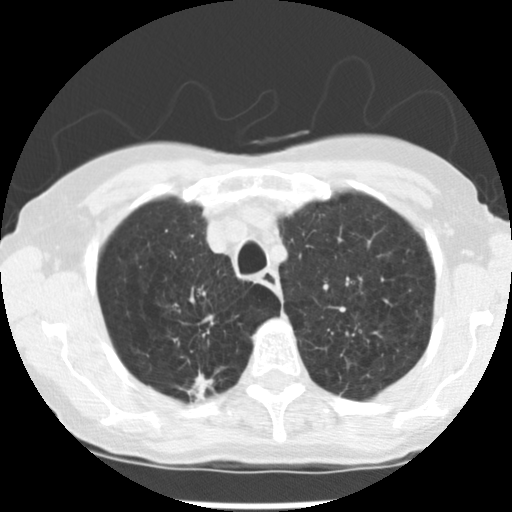
Axial slice from a low-dose chest CT screening exam, baseline screening round, lung window (W 1500 / L -600 HU), 2.5 mm slice thickness, standard (soft-tissue) reconstruction kernel (STANDARD). Female participant, aged 72 years at enrolment. Current smoker at enrolment.
Expert reader's lesion annotation, bounding box <182,364,231,406> (left, top, right, bottom; pixels). The screening reader recorded 3 non-calcified nodules or masses ≥4 mm on this exam (right upper lobe, left upper lobe, left lower lobe); which of them this box marks is not recorded. Official screen result: positive, change unspecified: nodule(s) >= 4 mm or enlarging nodule(s), mass(es), or other non-specific abnormalities suspicious for lung cancer.